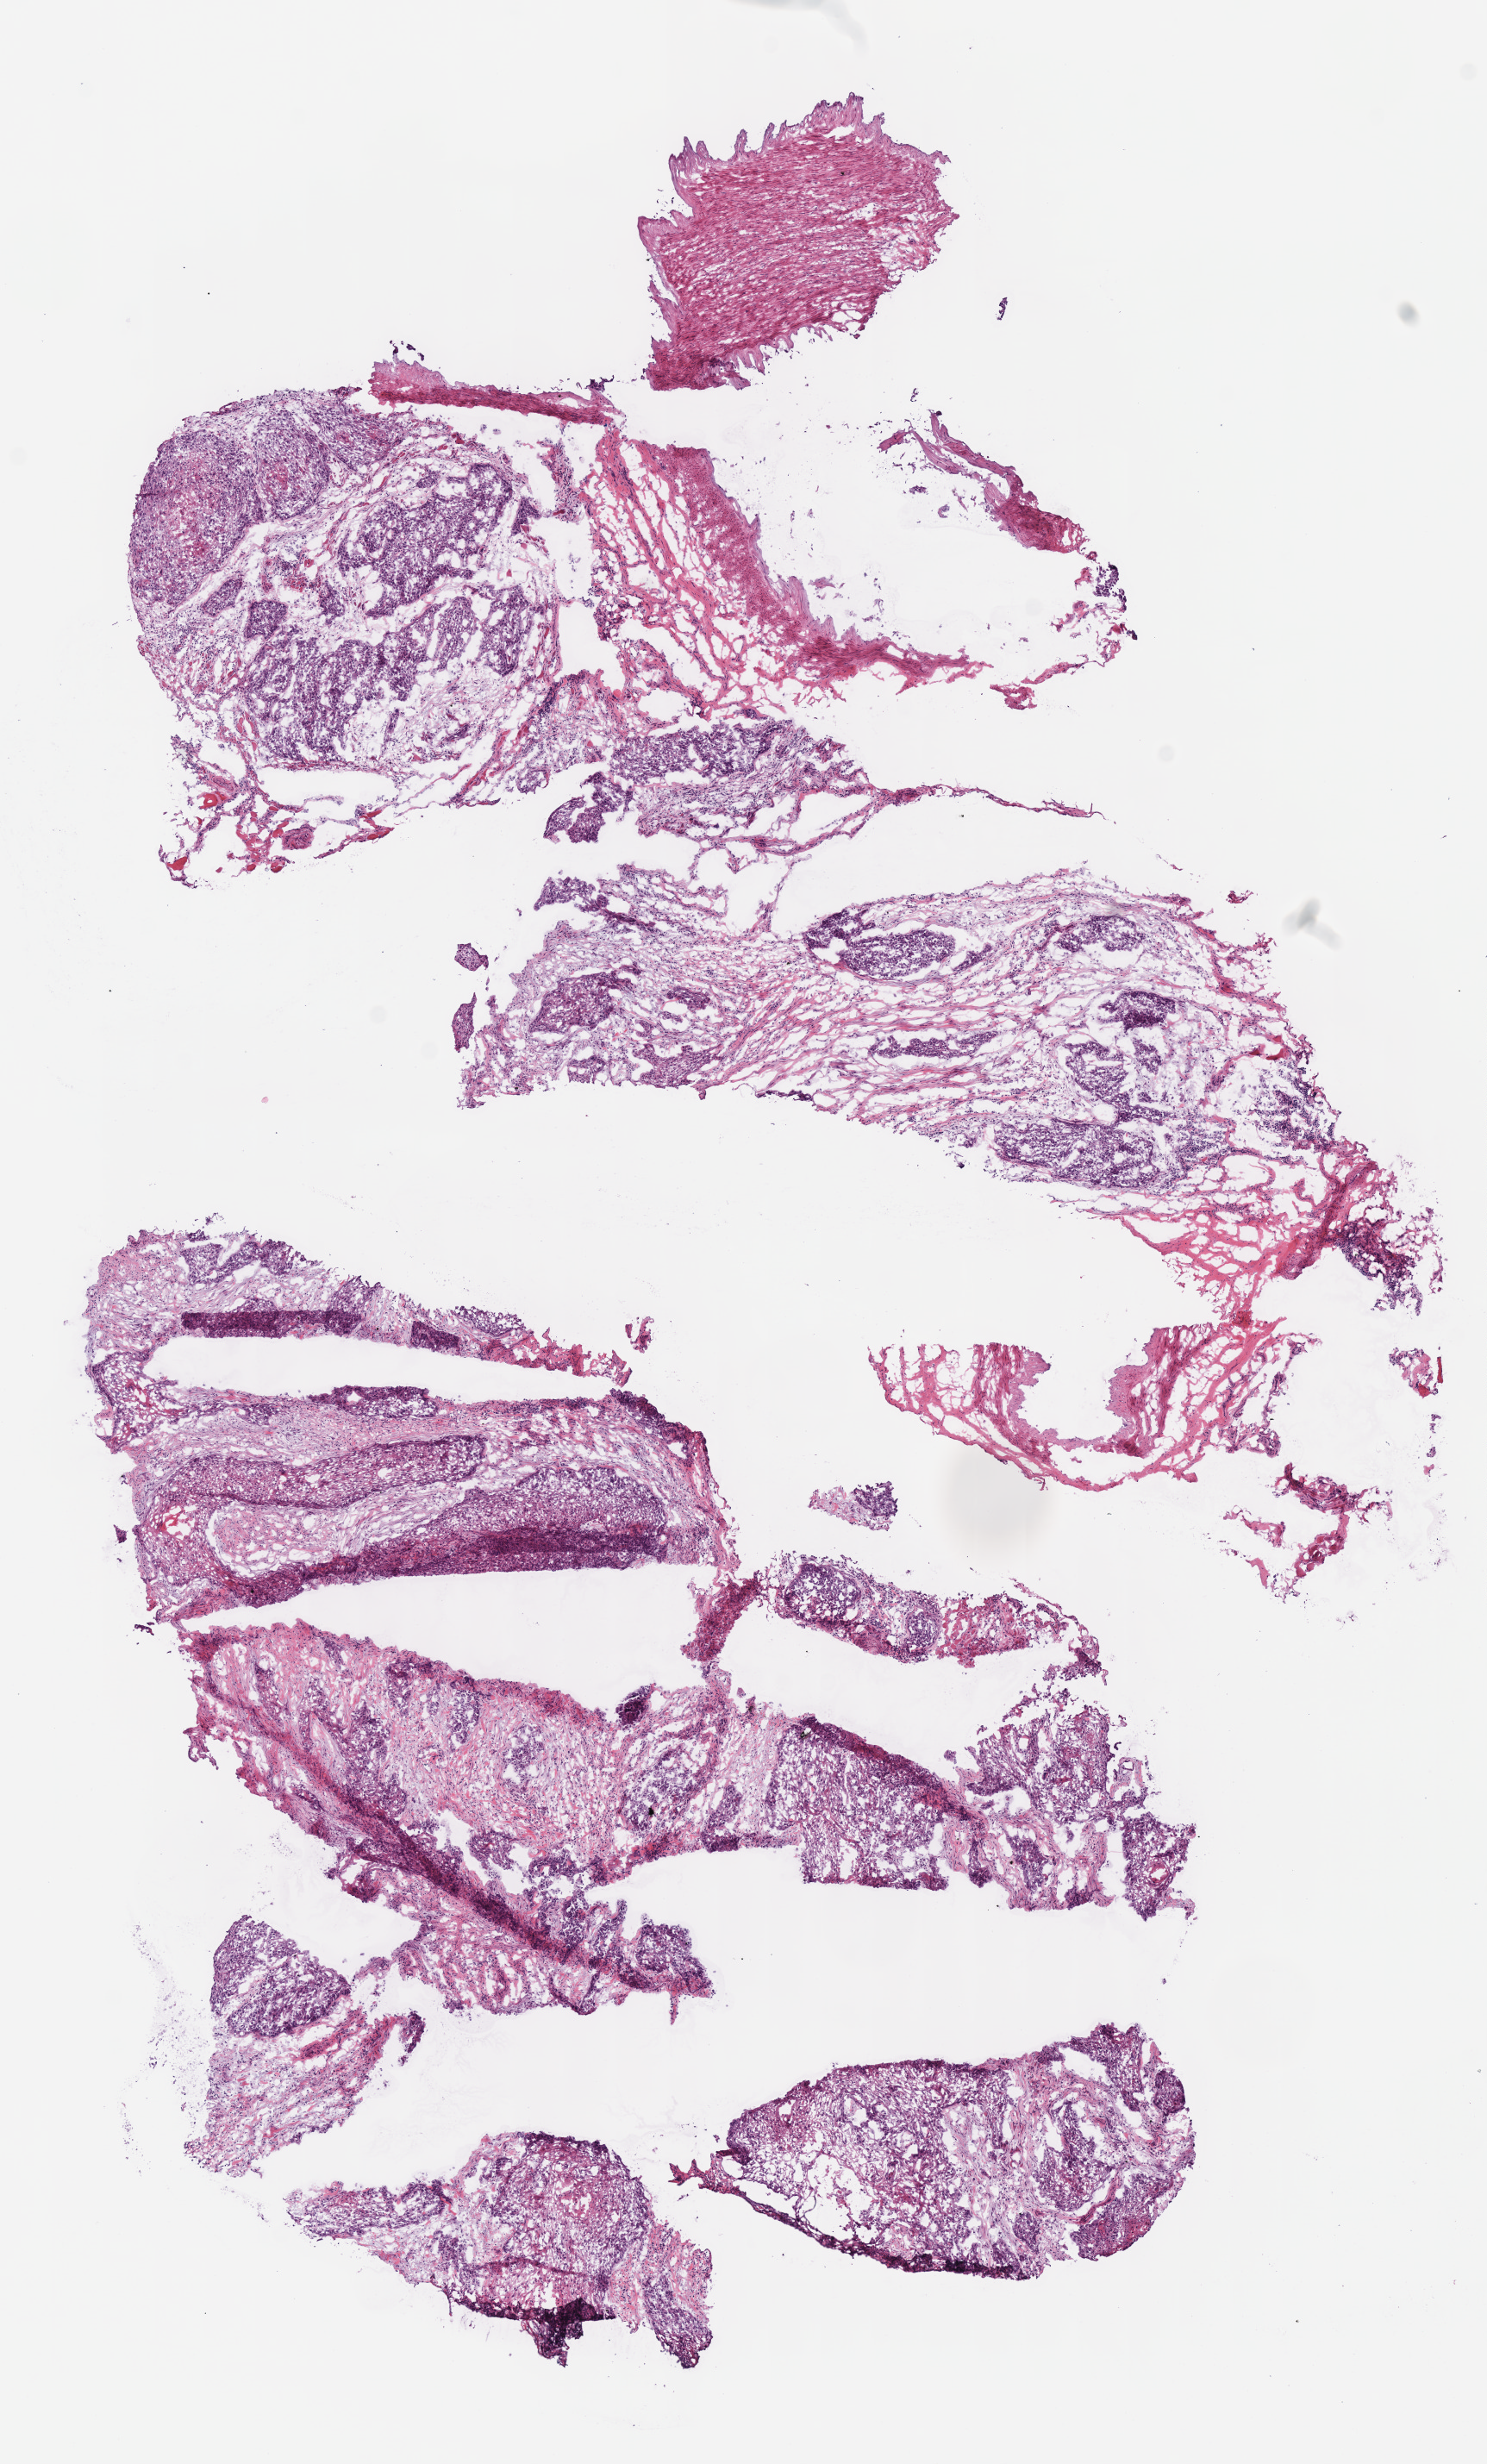
Whole-slide histology image, H&E, shown as a low-resolution overview of the whole scanned area (about 6.8 x 11.3 mm, acquisition: 40x scan). Frozen section from the bottom of the tissue portion. Sample: primary tumour, head and neck. Female patient; age at initial diagnosis 67 years. Histologic grade: G2 (moderately differentiated). Slide review estimates, as recorded: tumour cells 75%, tumour nuclei 75%, normal cells 0%, stromal cells 25%, necrosis 0%. Infiltration values recorded for this section: lymphocyte infiltration 5%, monocyte infiltration 0%, neutrophil infiltration 0%.
- AJCC pathologic stage: II (7th edition)
- histologic diagnosis: Squamous cell carcinoma, NOS (floor of mouth, NOS)
- laterality: right